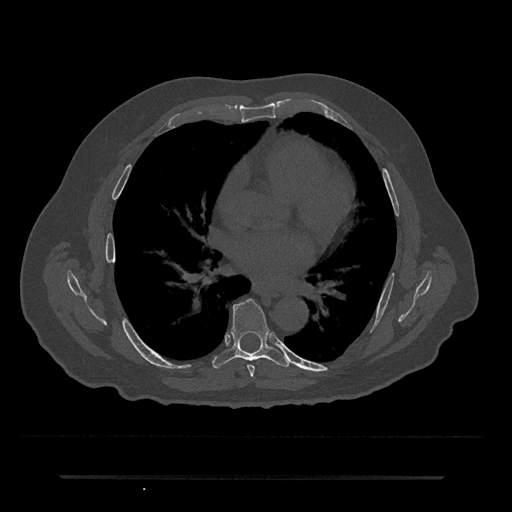
CT including the spine, one axial slice; slice 397 of 797 in the series (ordered by position); bone window (W 1800 / L 400 HU); 0.5 mm slice thickness; 512 × 512 image matrix, field of view 437 × 437 mm. Male patient, age 69 years. From the clinical record (not read from this slice): primary cancer: prostate.
Structures marked on this image (semi-automatically segmented with operator editing):
- T6 vertebra: bounding box <247,364,255,377> (left, top, right, bottom; pixels)
- T7 vertebra: <212,298,290,369>